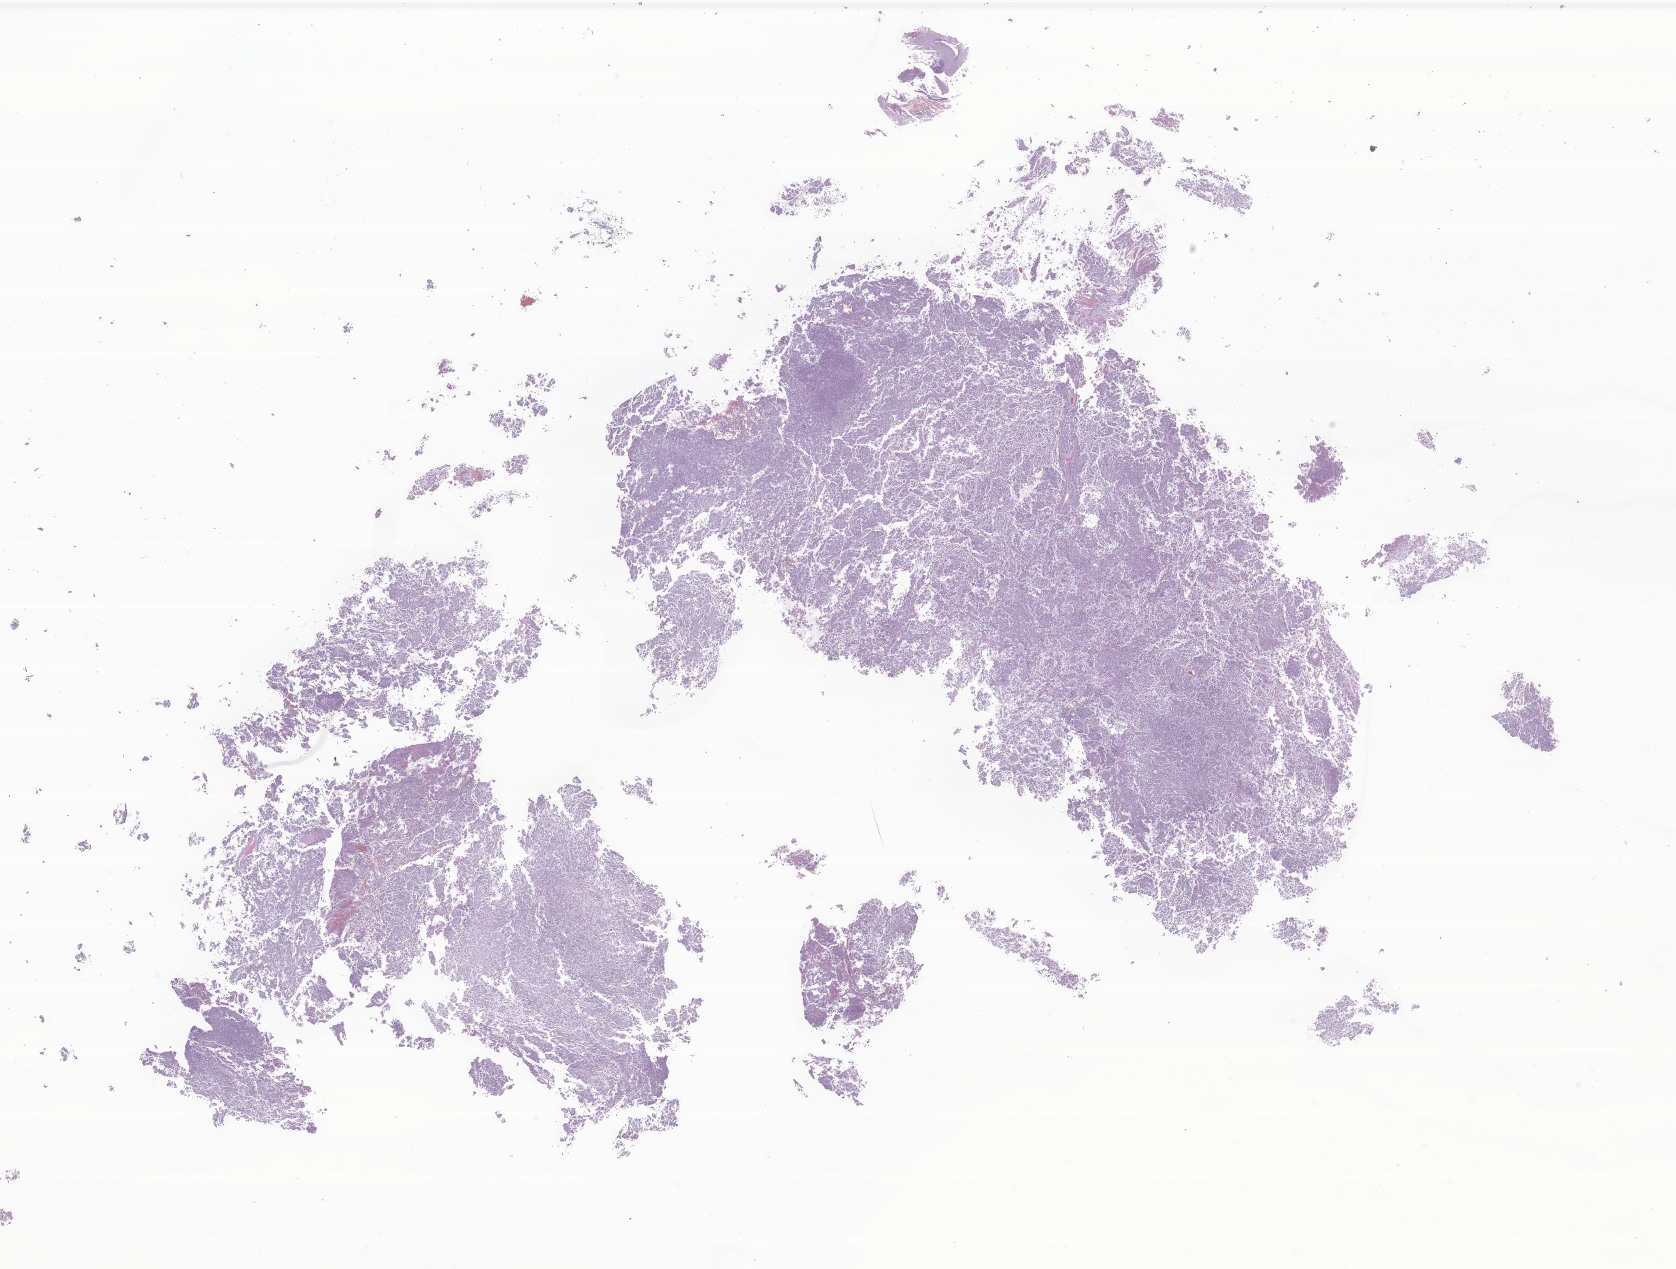
H&E whole-slide image of tumor tissue from the brain, low-resolution overview of the scanned area, about 28.3 x 21.4 mm, formalin-fixed paraffin-embedded section. Patient male; age 247 days.
* diagnosis (ICD-O-3 morphology term): Neoplasm, uncertain whether benign or malignant